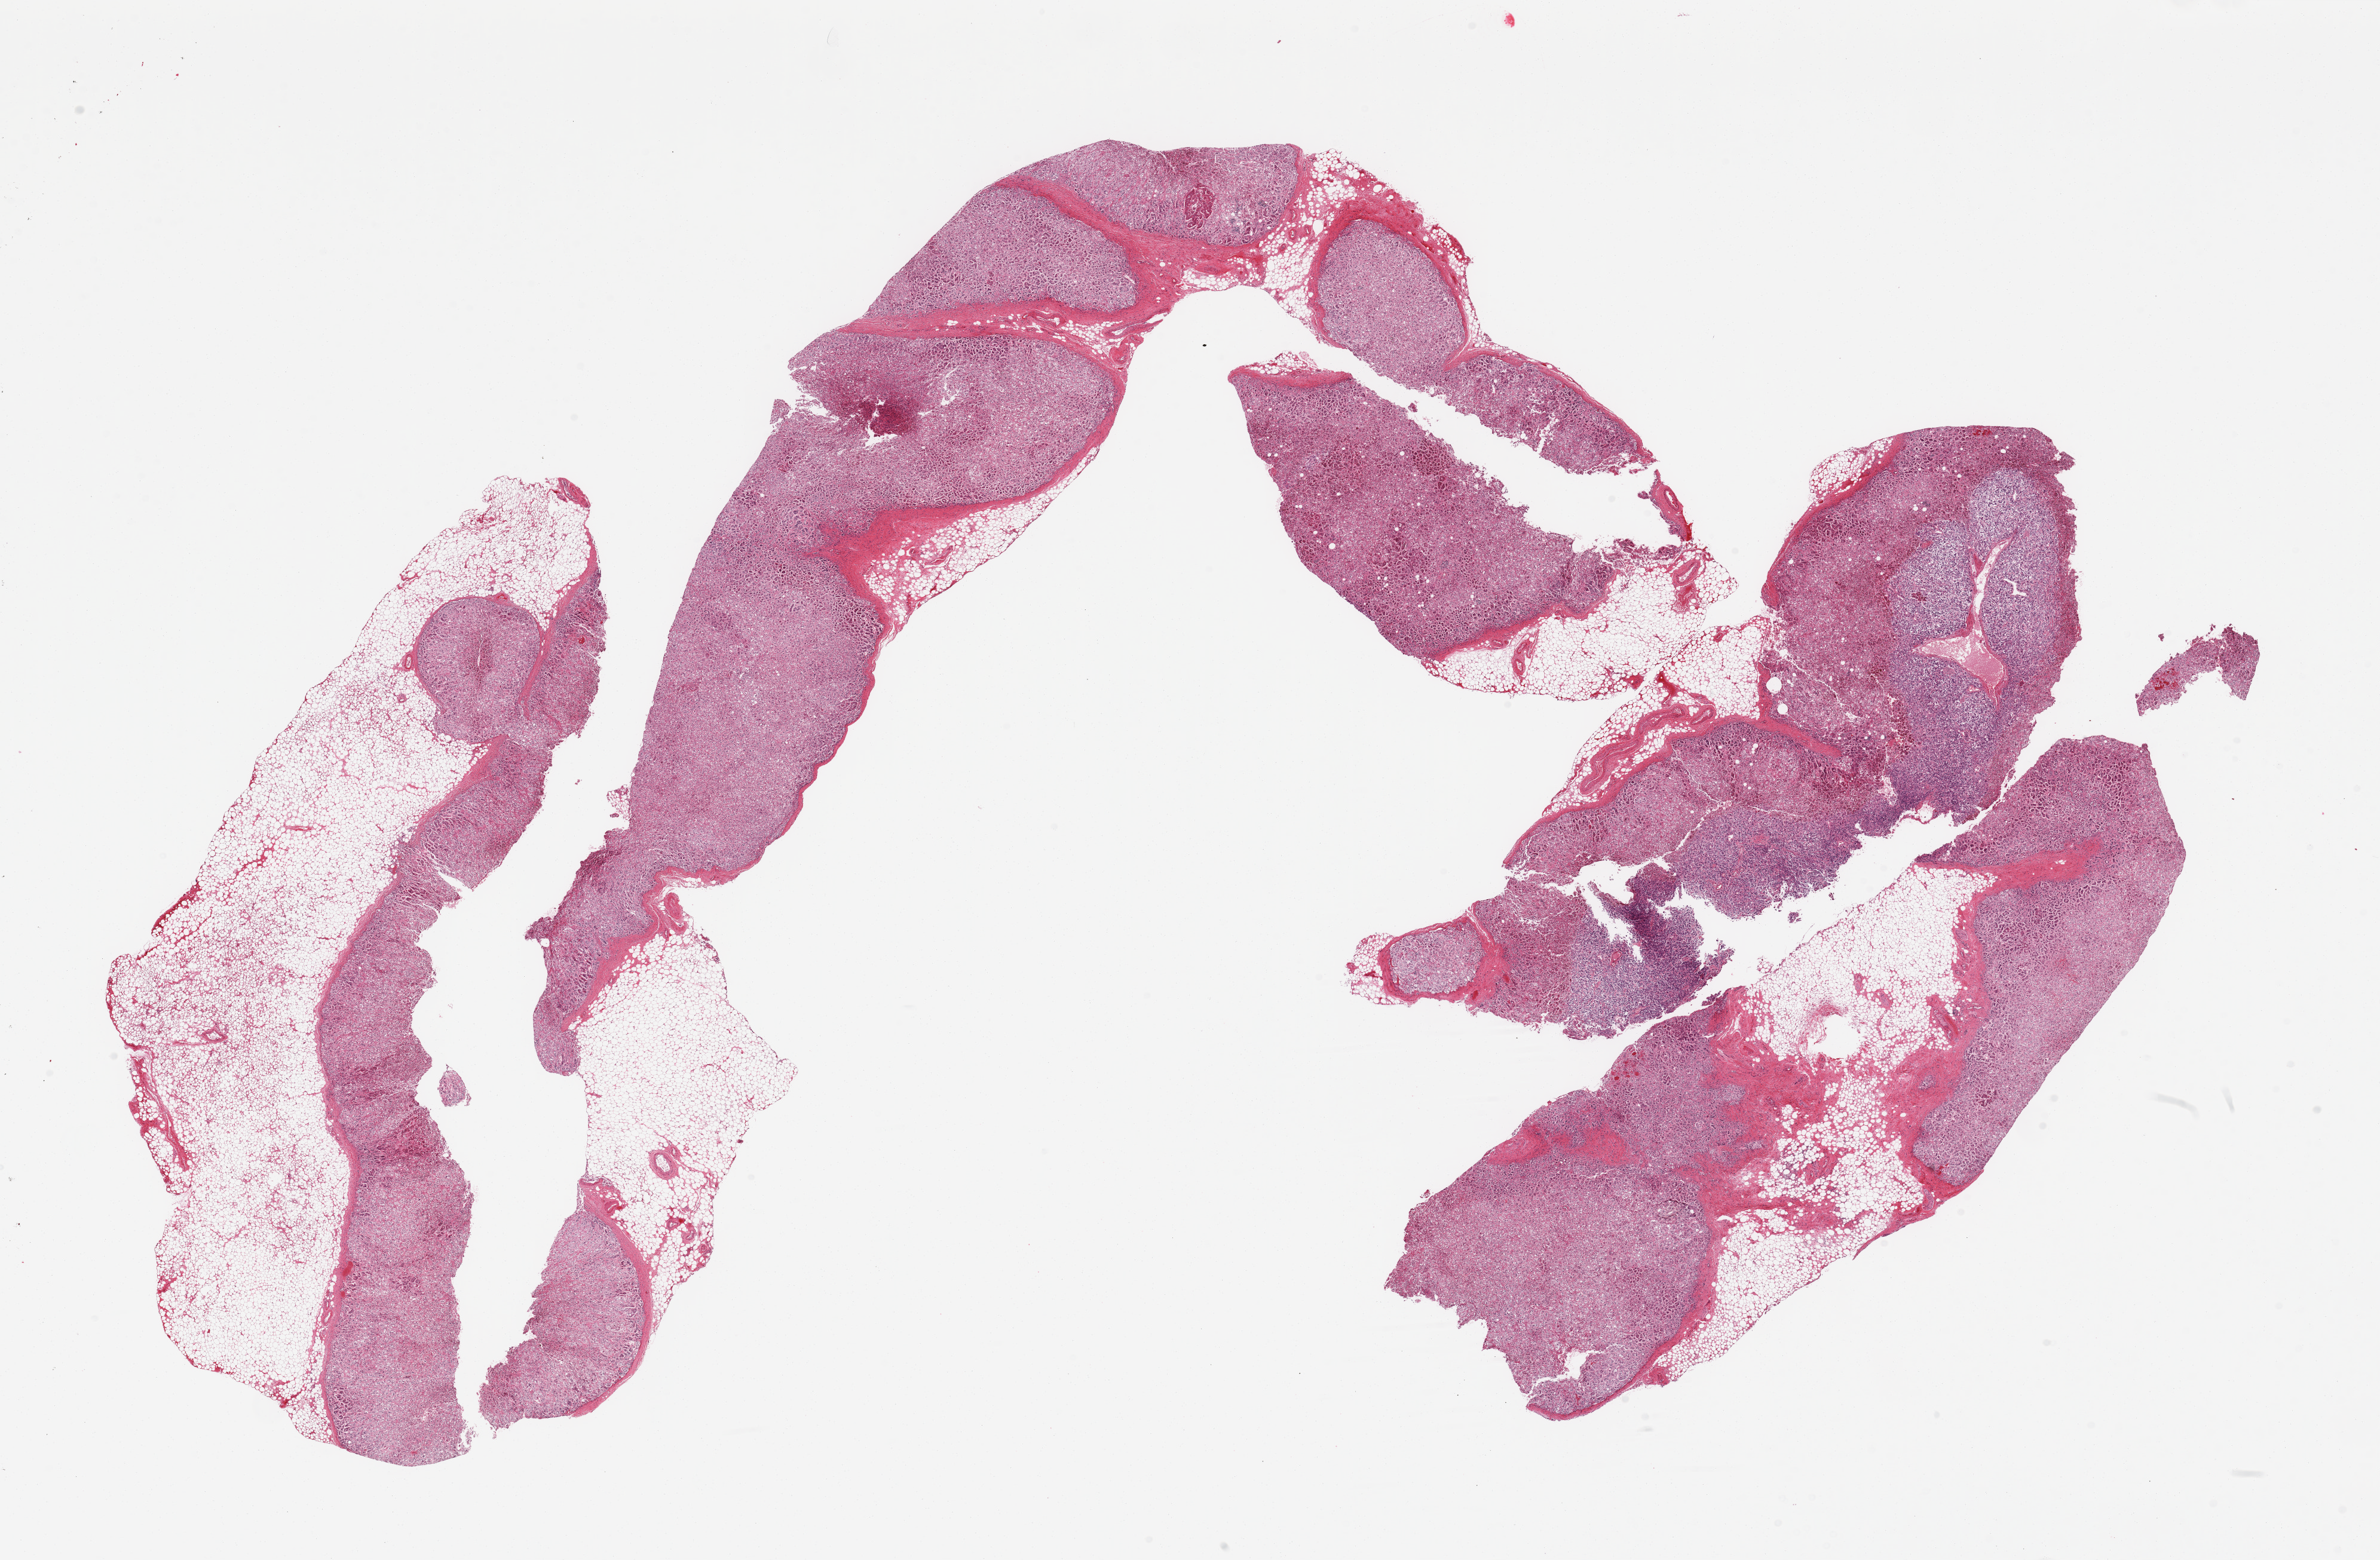
Whole-slide image, H&E stain, brightfield, whole scanned area (about 31.5 x 20.7 mm) shown as a low-resolution overview, PAXgene-fixed, paraffin-embedded tissue, target tissue: adrenal gland, donor tissue sample. Male donor.
* review note (as recorded): 2 pieces, cortex; ~30% adherent/interstitial fat